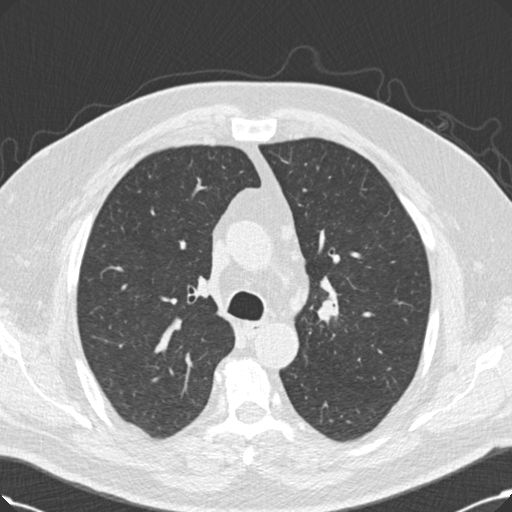
Low-dose screening chest CT, one axial slice; slice 152 of 214 in the series (ordered by position); reconstruction kernel B30f; 120 kVp; lung window (W 1500 / L -600 HU); 2 mm slice thickness; 512 × 512 image matrix.
Annotated regions visible in this slice (outlined manually by an expert reader):
- lesion 1 (tumor): bounding box [x1, y1, x2, y2] px = [318, 299, 339, 322]